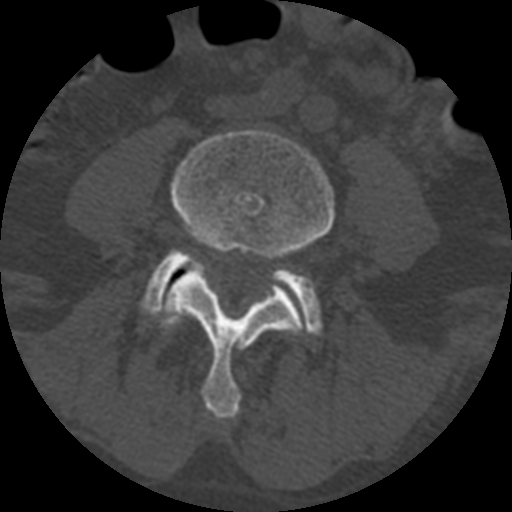
CT including the spine, one axial slice; position 274 of 399 along the scan axis; reconstruction kernel STANDARD; 120 kVp; bone window (W 1800 / L 400 HU); 512 × 512 image matrix. Patient age 71 years. Case-level facts recorded for this patient, not image findings: primary cancer: prostate.
Structures marked on this image (semi-automatic segmentation, software-assisted and operator-edited):
- L4 vertebra: bounding box <158,129,334,419> (left, top, right, bottom; pixels)
- L5 vertebra: <141,250,322,336>